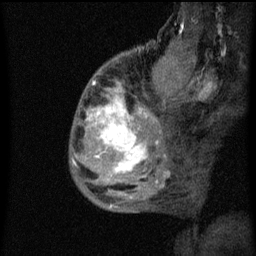
Breast MRI (dynamic contrast-enhanced), one sagittal slice. Position 17 of 60 along the scan axis. Dynamic contrast-enhanced series, image 2 of 3 at this slice position (ordered by acquisition). 1.5 T. TE 4.2 ms, TR 8 ms. 256 × 256 image matrix, field of view 180 × 180 mm. Patient: female, 50 years.
Structures marked on this image (semi-automatic segmentation, software-assisted and operator-edited):
- analysis volume of interest (the breast-tissue region the enhancement analysis was run in; not a lesion): bounding box [x1, y1, x2, y2] px = [70, 64, 141, 187]
- tumour enhancement mask (voxels above the 70 % enhancement threshold inside the analysis volume of interest): [76, 82, 141, 171]